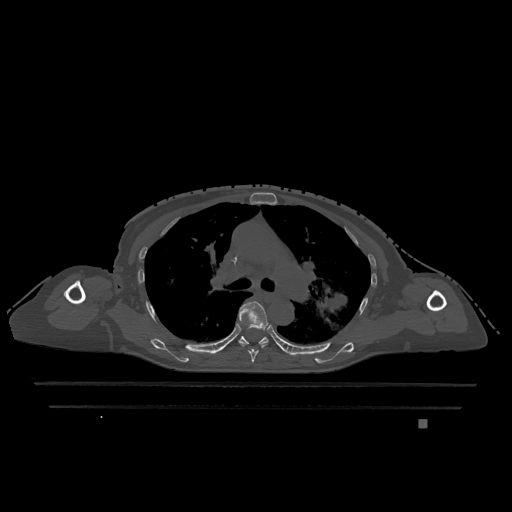
CT including the spine, one axial slice. Slice 815 of 1317 in the series (ordered by position). Bone window (W 1800 / L 400 HU). 0.5 mm slice thickness. 512 × 512 image matrix. Female patient, age 74 years. From the clinical record (not read from this slice): primary cancer: lung.
Annotated regions visible in this slice (semi-automatic segmentation, software-assisted and operator-edited):
- T5 vertebra: box from (x=239, y=301) to (x=268, y=362) px
- T6 vertebra: (x=238, y=336)–(x=269, y=345)